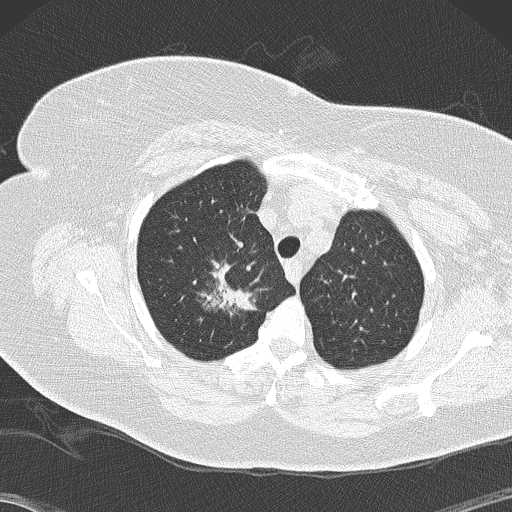
Axial slice from a low-dose chest CT screening exam. Second annual screen. Lung window (W 1500 / L -600 HU). 2 mm slice thickness. Lung (sharp) reconstruction kernel (B50f). Female participant, aged 72 years at enrolment. Former smoker at enrolment.
Lesion marked by an expert reader, bounding box (x1, y1, x2, y2) in pixels: (180, 242, 262, 327). The screening reader recorded 4 non-calcified nodules or masses ≥4 mm on this exam; which of them this box marks is not recorded. Participant outcome: lung cancer diagnosed 52 days after this screen — bronchiolo-alveolar adenocarcinoma, NOS, right upper lobe, stage IIIB (AJCC 6th edition), 45 mm at pathology.